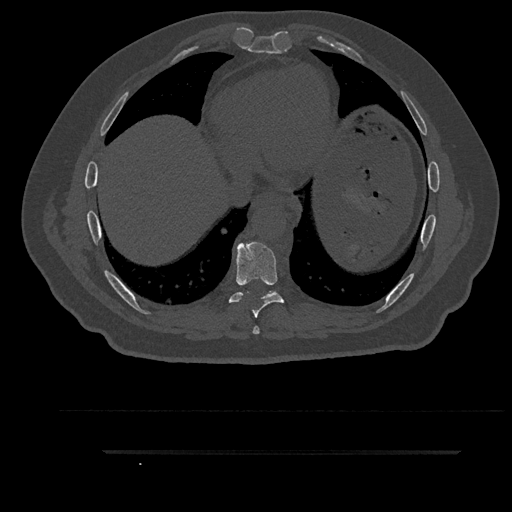
CT including the spine, one axial slice. Slice 472 of 797 in the series (ordered by position). 120 kVp. Bone window (W 1800 / L 400 HU). 512 × 512 image matrix, field of view 432 × 432 mm. Male patient, age 63 years. Case-level facts recorded for this patient, not image findings: primary cancer: renal.
Outlined on this slice (semi-automatic segmentation, software-assisted and operator-edited):
- T7 vertebra: bounding box [x1, y1, x2, y2] px = [252, 326, 260, 335]
- T8 vertebra: [229, 242, 284, 318]